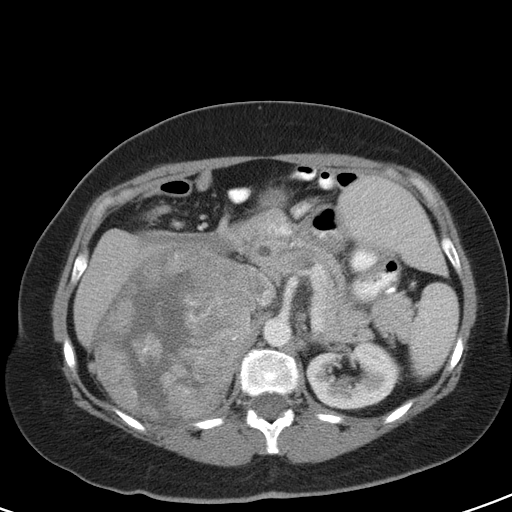
Contrast-enhanced abdominal CT, one axial slice; 120 kVp; intravenous contrast given; soft-tissue window (W 400 / L 40 HU); 5 mm slice thickness; 512 × 512 image matrix, field of view 356 × 356 mm. Female patient, age 51 years. From the clinical record (not read from this slice): diagnosis: adrenocortical carcinoma; tumour side: right adrenal.
Annotated regions visible in this slice (semi-automatic segmentation, software-assisted and operator-edited):
- mass: box from (x=95, y=249) to (x=254, y=420) px